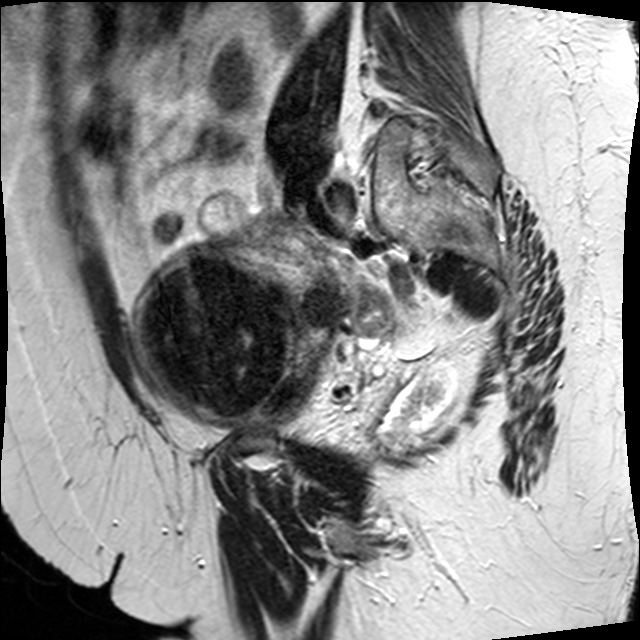
Pelvic MRI for cervical cancer, one sagittal slice. Slice 10 of 34 in the series (ordered by position). T2-weighted. 1.5 T. TE 89 ms, TR 3320 ms. 4 mm slice thickness. 640 × 640 image matrix, field of view 260 × 260 mm. Female patient, age 50 years.
Annotated regions visible in this slice (manually delineated by an expert):
- uterus and cervix: bounding box (x1, y1, x2, y2) in pixels: (128, 240, 445, 438)